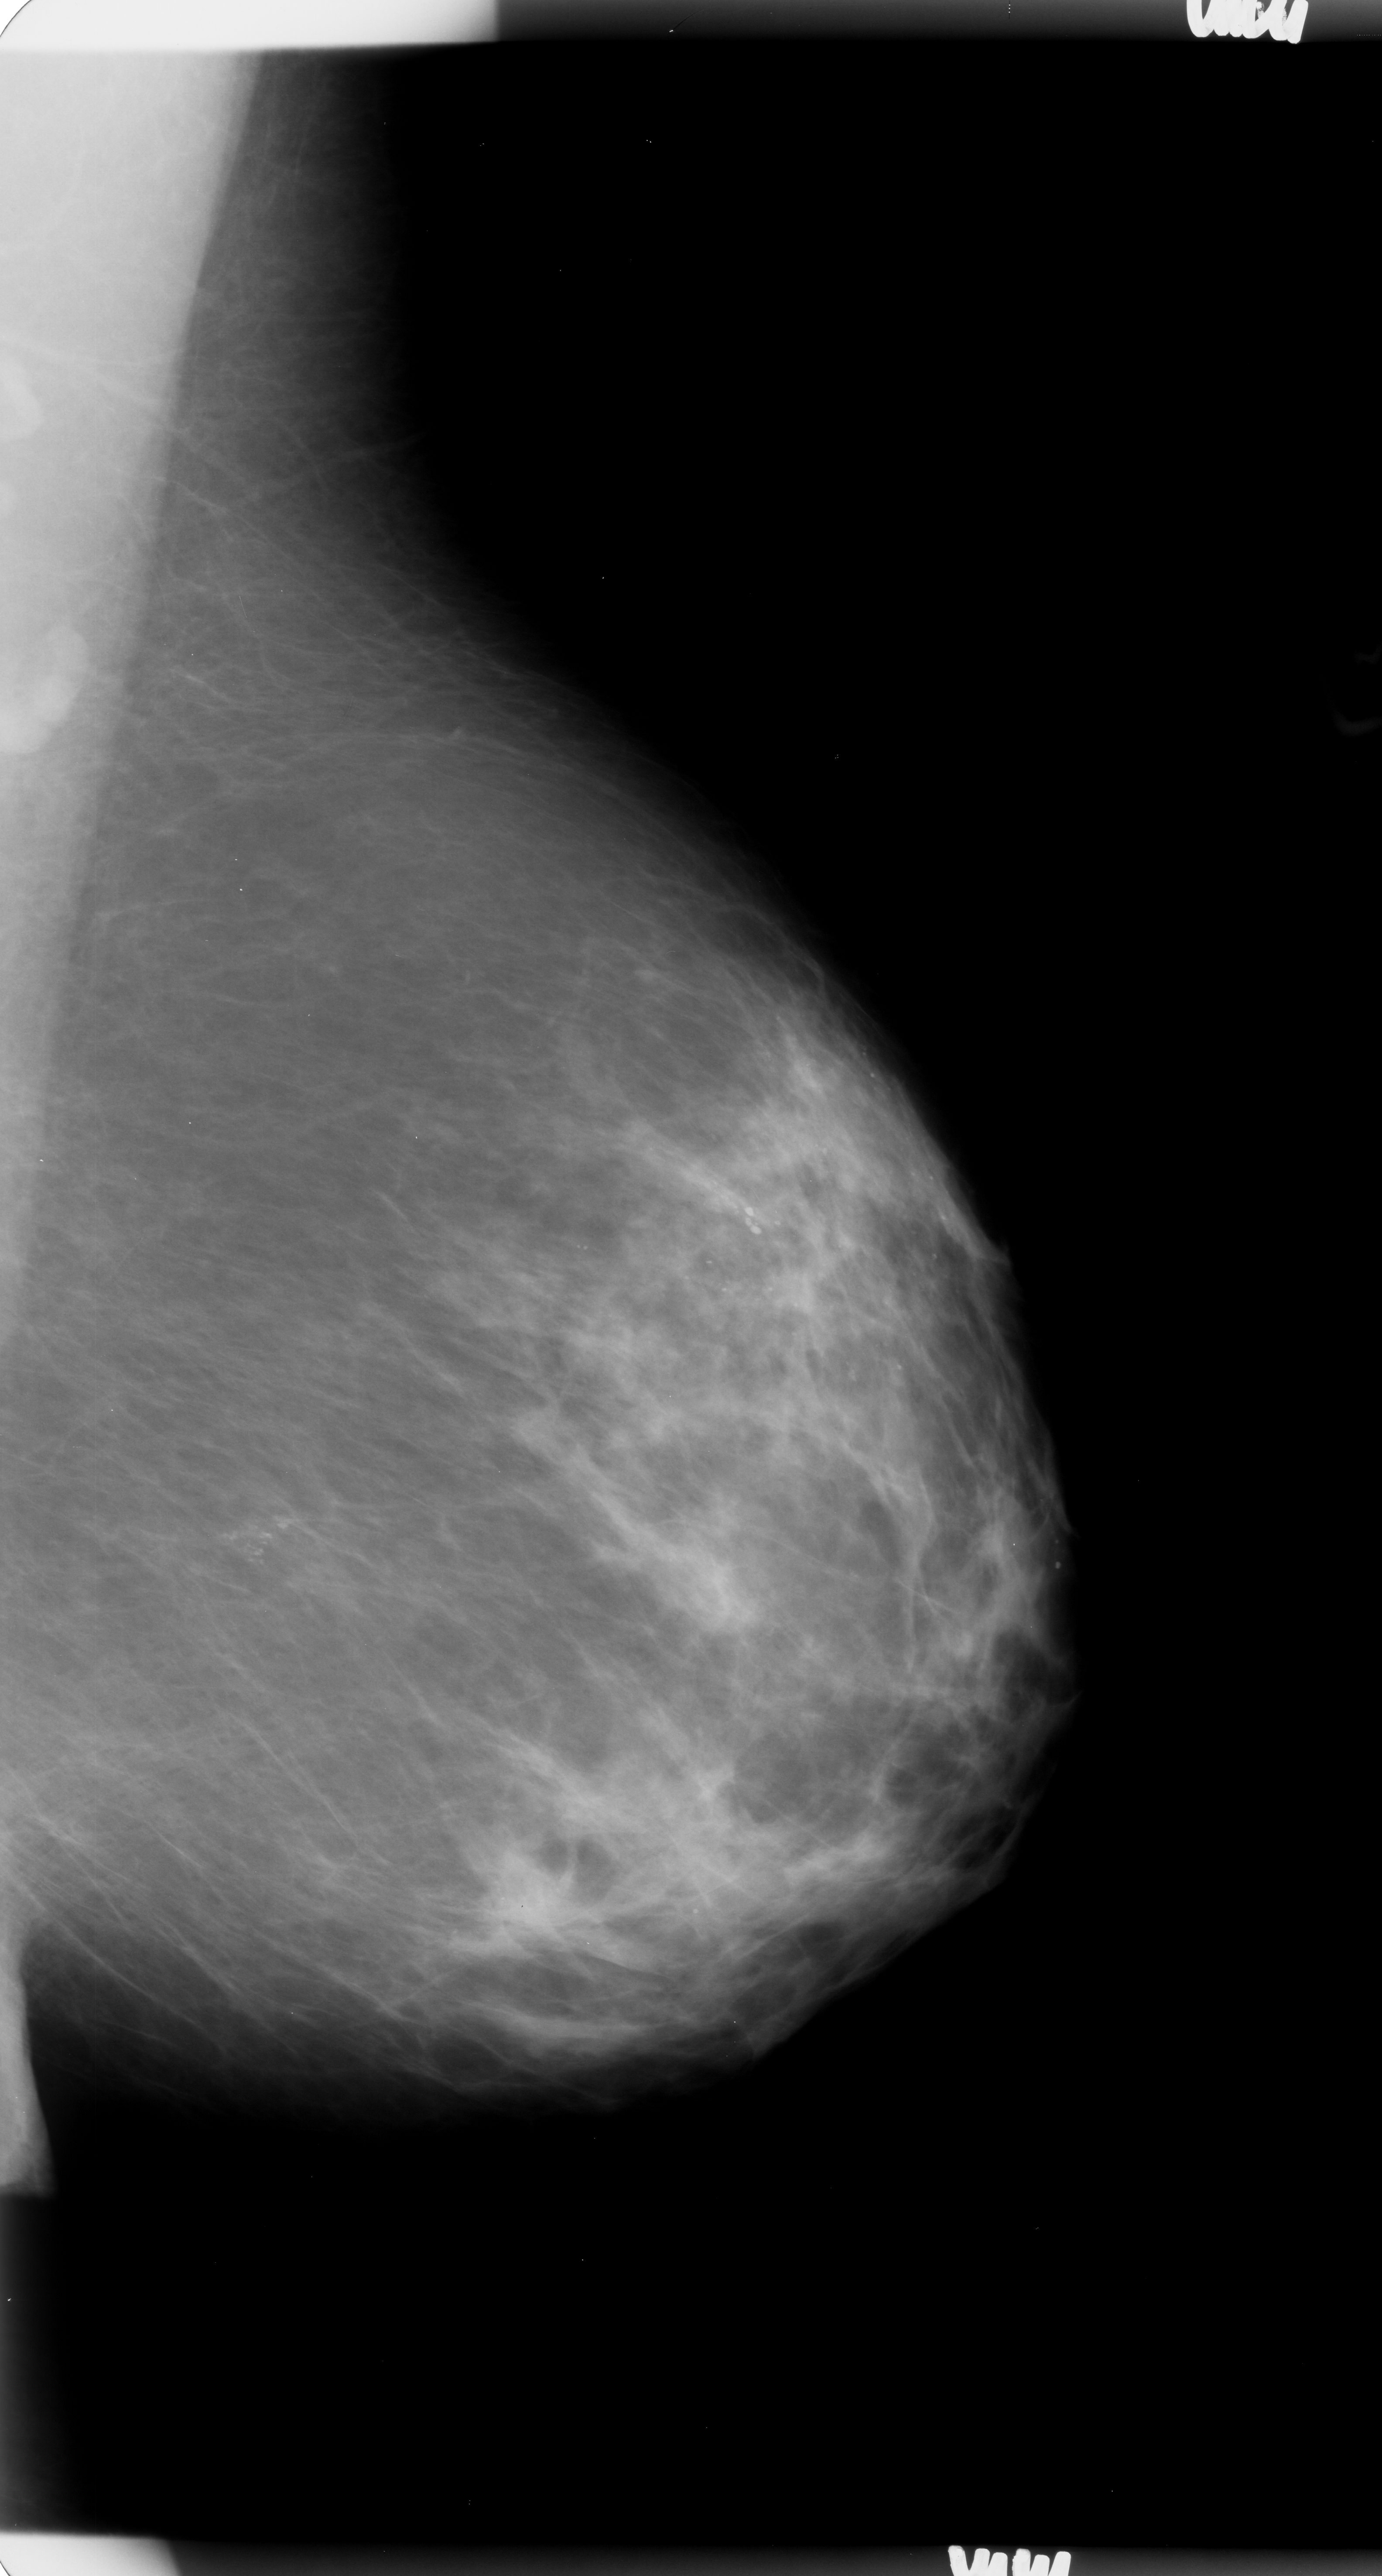
Mammogram (digitized film). Left breast. MLO view. BI-RADS breast density category 2 (scale 1–4). 1382 × 2576 image matrix.
Expert-marked regions of interest on this film, with their recorded descriptors:
- calcifications, morphology pleomorphic, distribution clustered; BI-RADS assessment category 4; subtlety rating 4 on a 1 (subtle) to 5 (obvious) scale; pathology result (as recorded, not read from the image): benign: bounding box <195,1455,332,1607> (left, top, right, bottom; pixels)